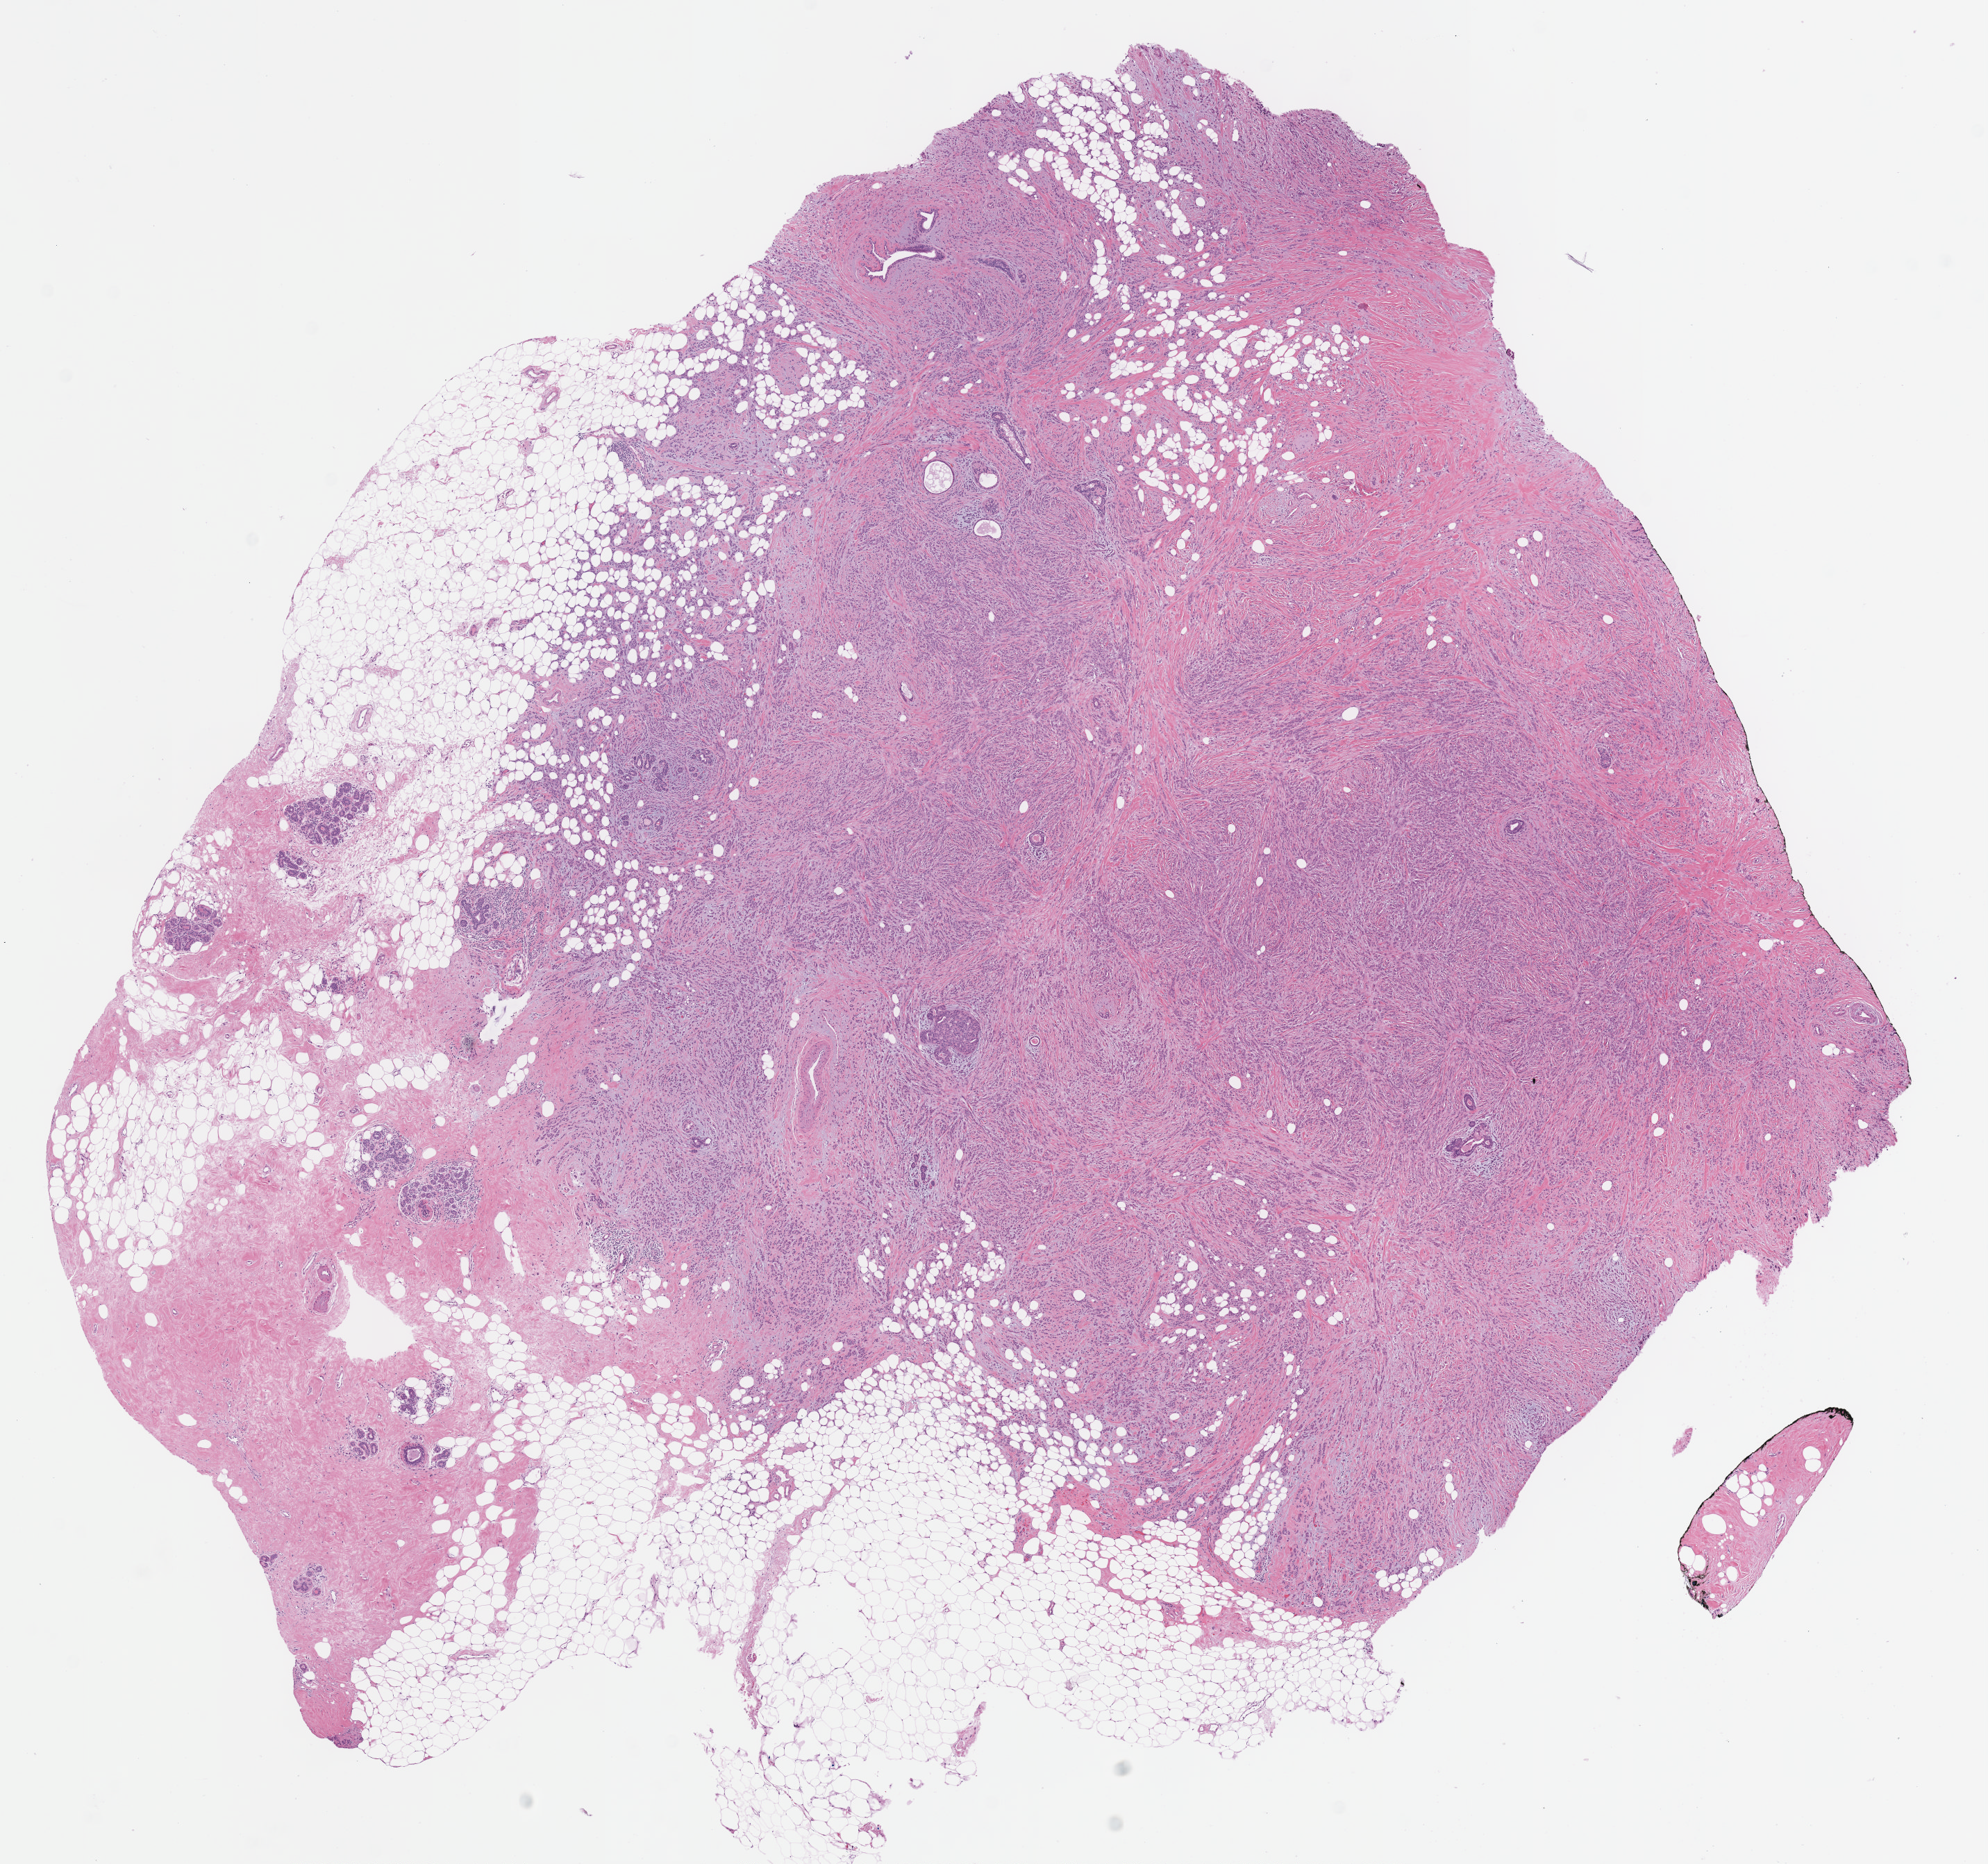
Whole-slide histology image, H&E, a low-resolution overview of the entire scanned area, about 11.3 x 10.6 mm, formalin-fixed paraffin-embedded (FFPE) diagnostic section, primary tumour sample from the breast. Female patient; age at initial diagnosis 79 years.
Pathologic diagnosis: Lobular carcinoma, NOS. TNM: T2 N1mi MX. AJCC pathologic stage: IIB (7th edition).